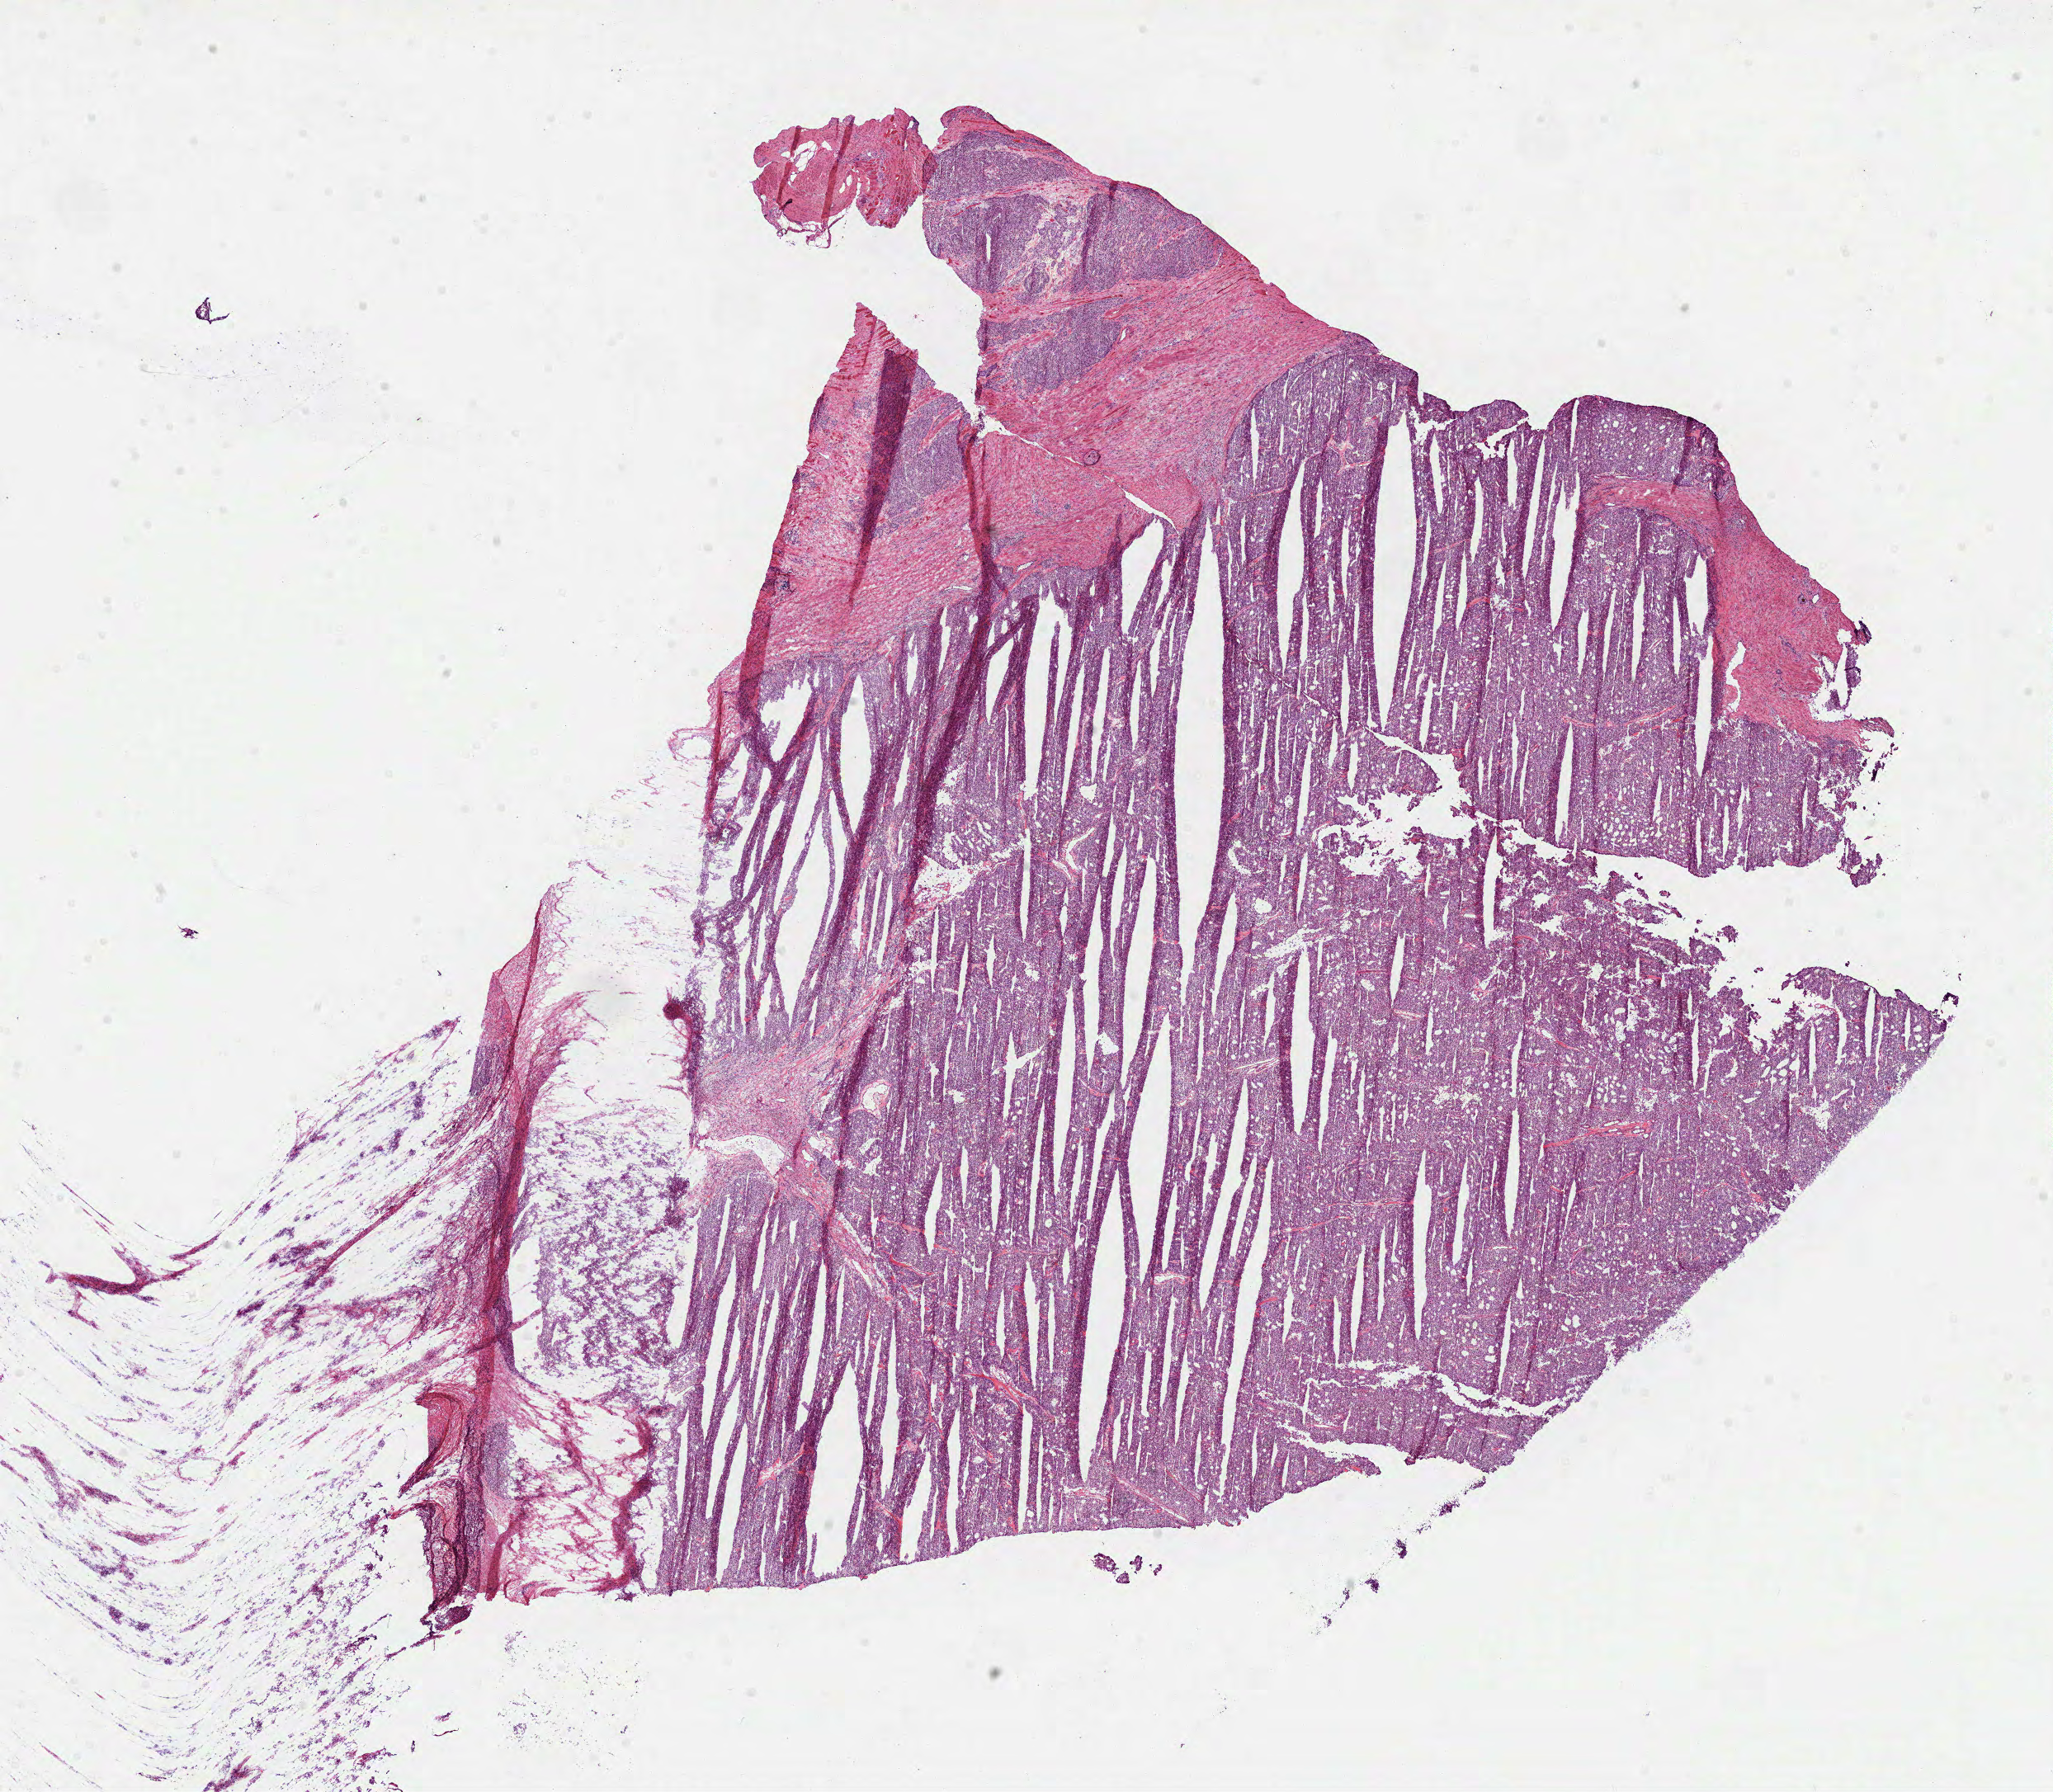
Digitized H&E-stained tissue section (whole slide), low-resolution overview of the scanned area, about 20.1 x 17.5 mm (slide scanned at 40x); frozen section from the top of the tissue portion; primary tumour sample from the prostate. Patient: male, age at initial diagnosis 66 years. Gleason score: 7 (4+3). Slide review estimates, as recorded: tumour cells 90%, tumour nuclei 95%, normal cells 3%, stromal cells 7%, necrosis 0%. Inflammatory infiltration, as recorded: lymphocyte infiltration 0%, monocyte infiltration 0%, neutrophil infiltration 0%.
Pathologic diagnosis: Acinar cell carcinoma (prostate gland). Lymph nodes positive (case pathology): 0 of 14 examined.